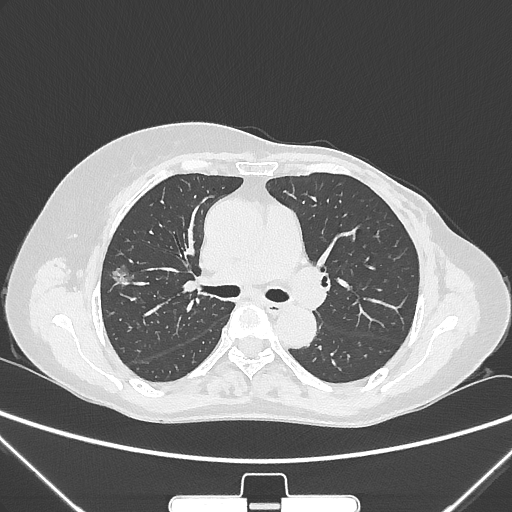
Chest CT, one axial slice. Slice 157 of 265 in the series (ordered by position). Reconstruction kernel IMR1,SharpPlus. 120 kVp. Lung window (W 1500 / L -600 HU). 1 mm slice thickness. 512 × 512 image matrix. Patient: female, 64 years. Case-level facts recorded for this patient, not image findings: clinical TNM (as recorded): T1c N0 M0; histopathological grade: G1-2.
Outlined on this slice (bounding box drawn by a radiologist):
- lung tumour (recorded histology: adenocarcinoma): bounding box [x1, y1, x2, y2] px = [111, 261, 140, 298]